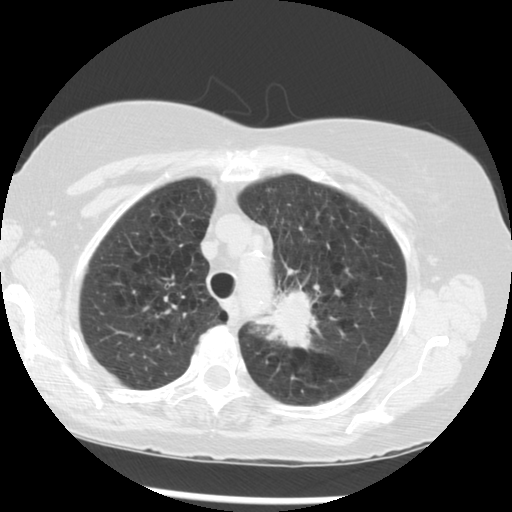
Axial slice from a low-dose chest CT screening exam; third annual screen; lung window (W 1500 / L -600 HU); 2.5 mm slice thickness; 120 kVp; slice 221 of 283 in the series. Female, age 70 years at enrolment. Current smoker at enrolment.
• Expert reader's lesion annotation, bounding box [x1, y1, x2, y2] px = [261, 273, 356, 362].
• Reader record for this screening exam (exam-level; its link to the box is not recorded): non-calcified nodule or mass ≥4 mm, left upper lobe, 32 × 26 mm, spiculated (stellate) margins, soft tissue attenuation, pre-existing on the prior screen: yes; interval growth: yes.
• Official screen result: positive, other.
• Lung cancer was diagnosed 24 days after this screen: neoplasm, malignant, left upper lobe, stage IIIB (AJCC 6th edition), 40 mm at pathology.